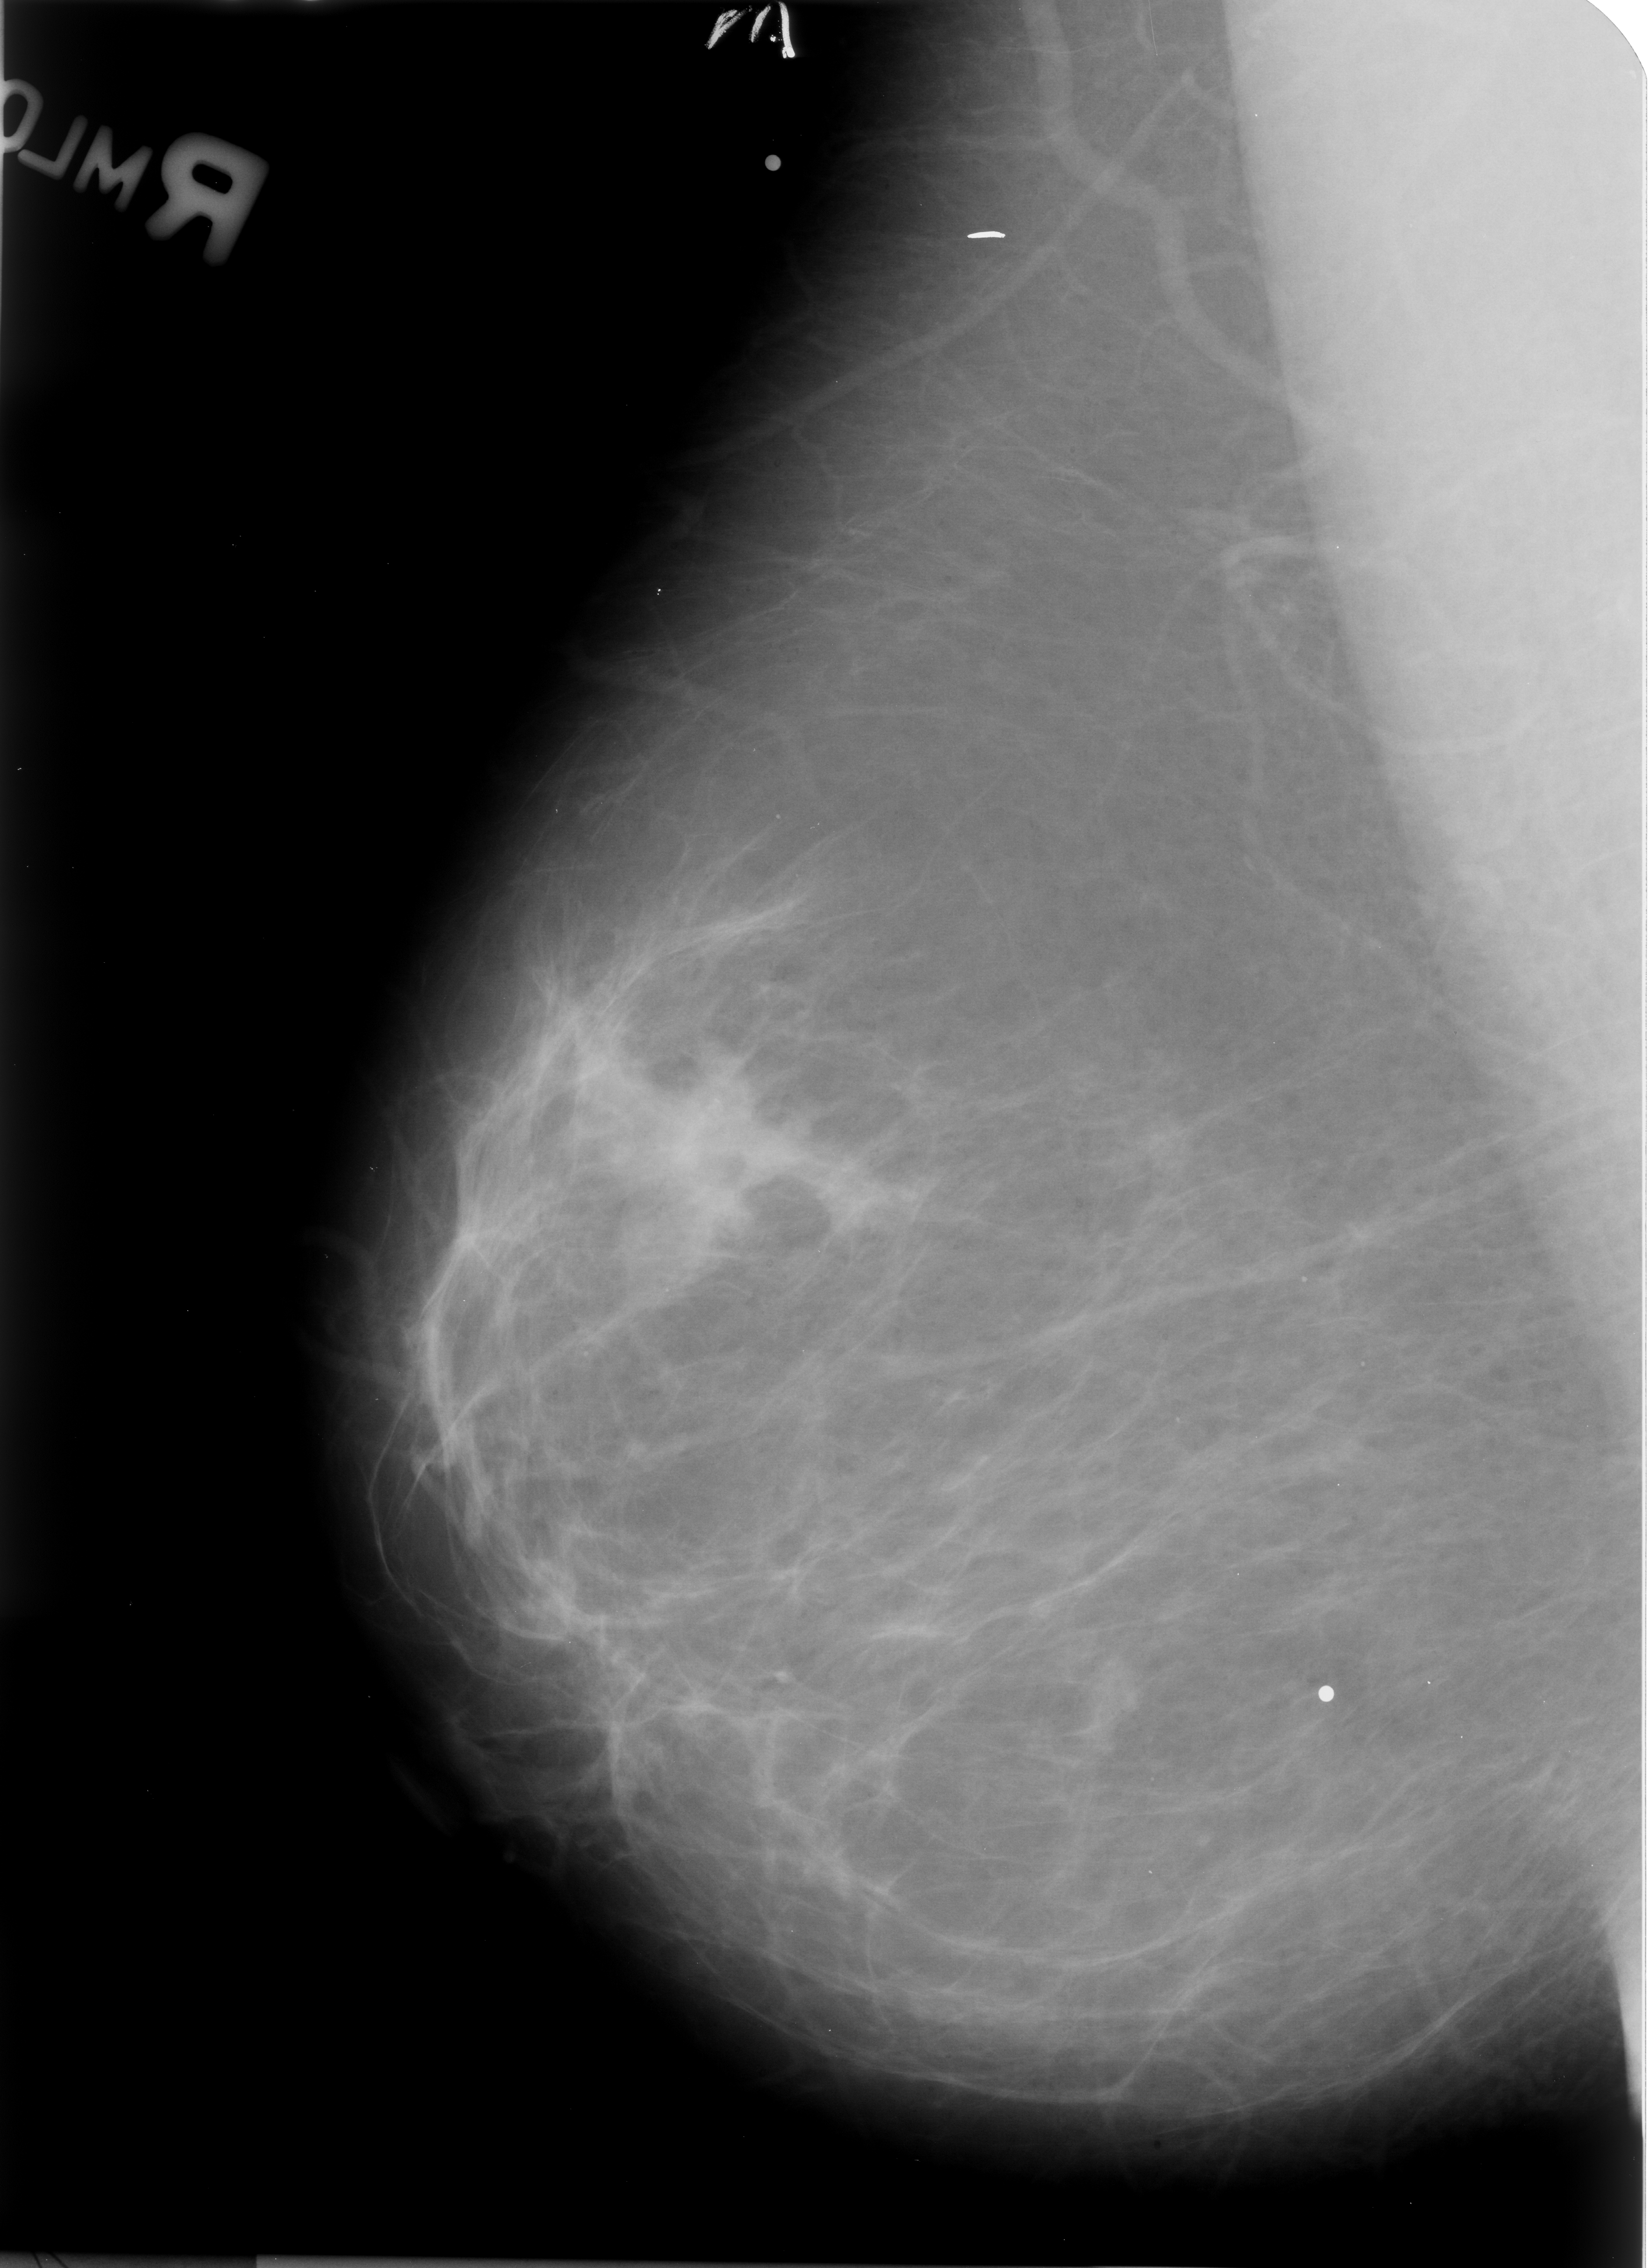
Scanned film-screen mammogram; right breast; MLO view; BI-RADS breast density category 1 (scale 1–4); 1649 × 2268 image matrix.
Marked abnormalities (boxes around the expert regions of interest):
- mass, shape irregular / architectural distortion, margins ill defined / spiculated; BI-RADS assessment category 4; pathology (as recorded): malignant: bounding box <622,1078,822,1268> (left, top, right, bottom; pixels)